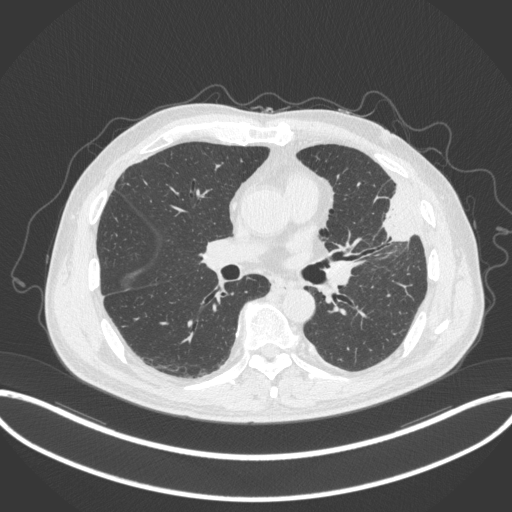
Chest CT, one axial slice; slice 177 of 382 in the series (ordered by position); reconstruction kernel B31f; lung window (W 1500 / L -600 HU); 1 mm slice thickness; 512 × 512 image matrix, field of view 415 × 415 mm. Male patient, age 64 years. From the clinical record (not read from this slice): clinical TNM (as recorded): T4 N1 M0.
Structures marked on this image (bounding box drawn by a radiologist):
- lung tumour (recorded histology: adenocarcinoma): bounding box [x1, y1, x2, y2] px = [378, 181, 417, 243]